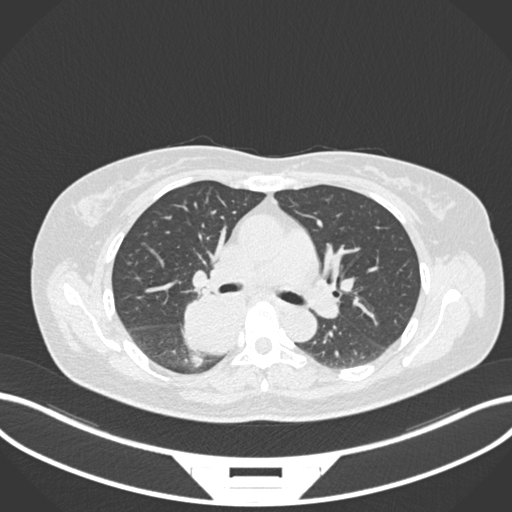
Chest CT, one axial slice; slice 612 of 677 in the series (ordered by position); 120 kVp; lung window (W 1500 / L -600 HU); 512 × 512 image matrix, field of view 400 × 400 mm. Patient: female, 54 years. From the clinical record (not read from this slice): clinical TNM (as recorded): T4 N0 M0.
Annotated regions visible in this slice (bounding box drawn by a radiologist):
- lung tumour (recorded histology: adenocarcinoma): box from (x=180, y=285) to (x=252, y=356) px